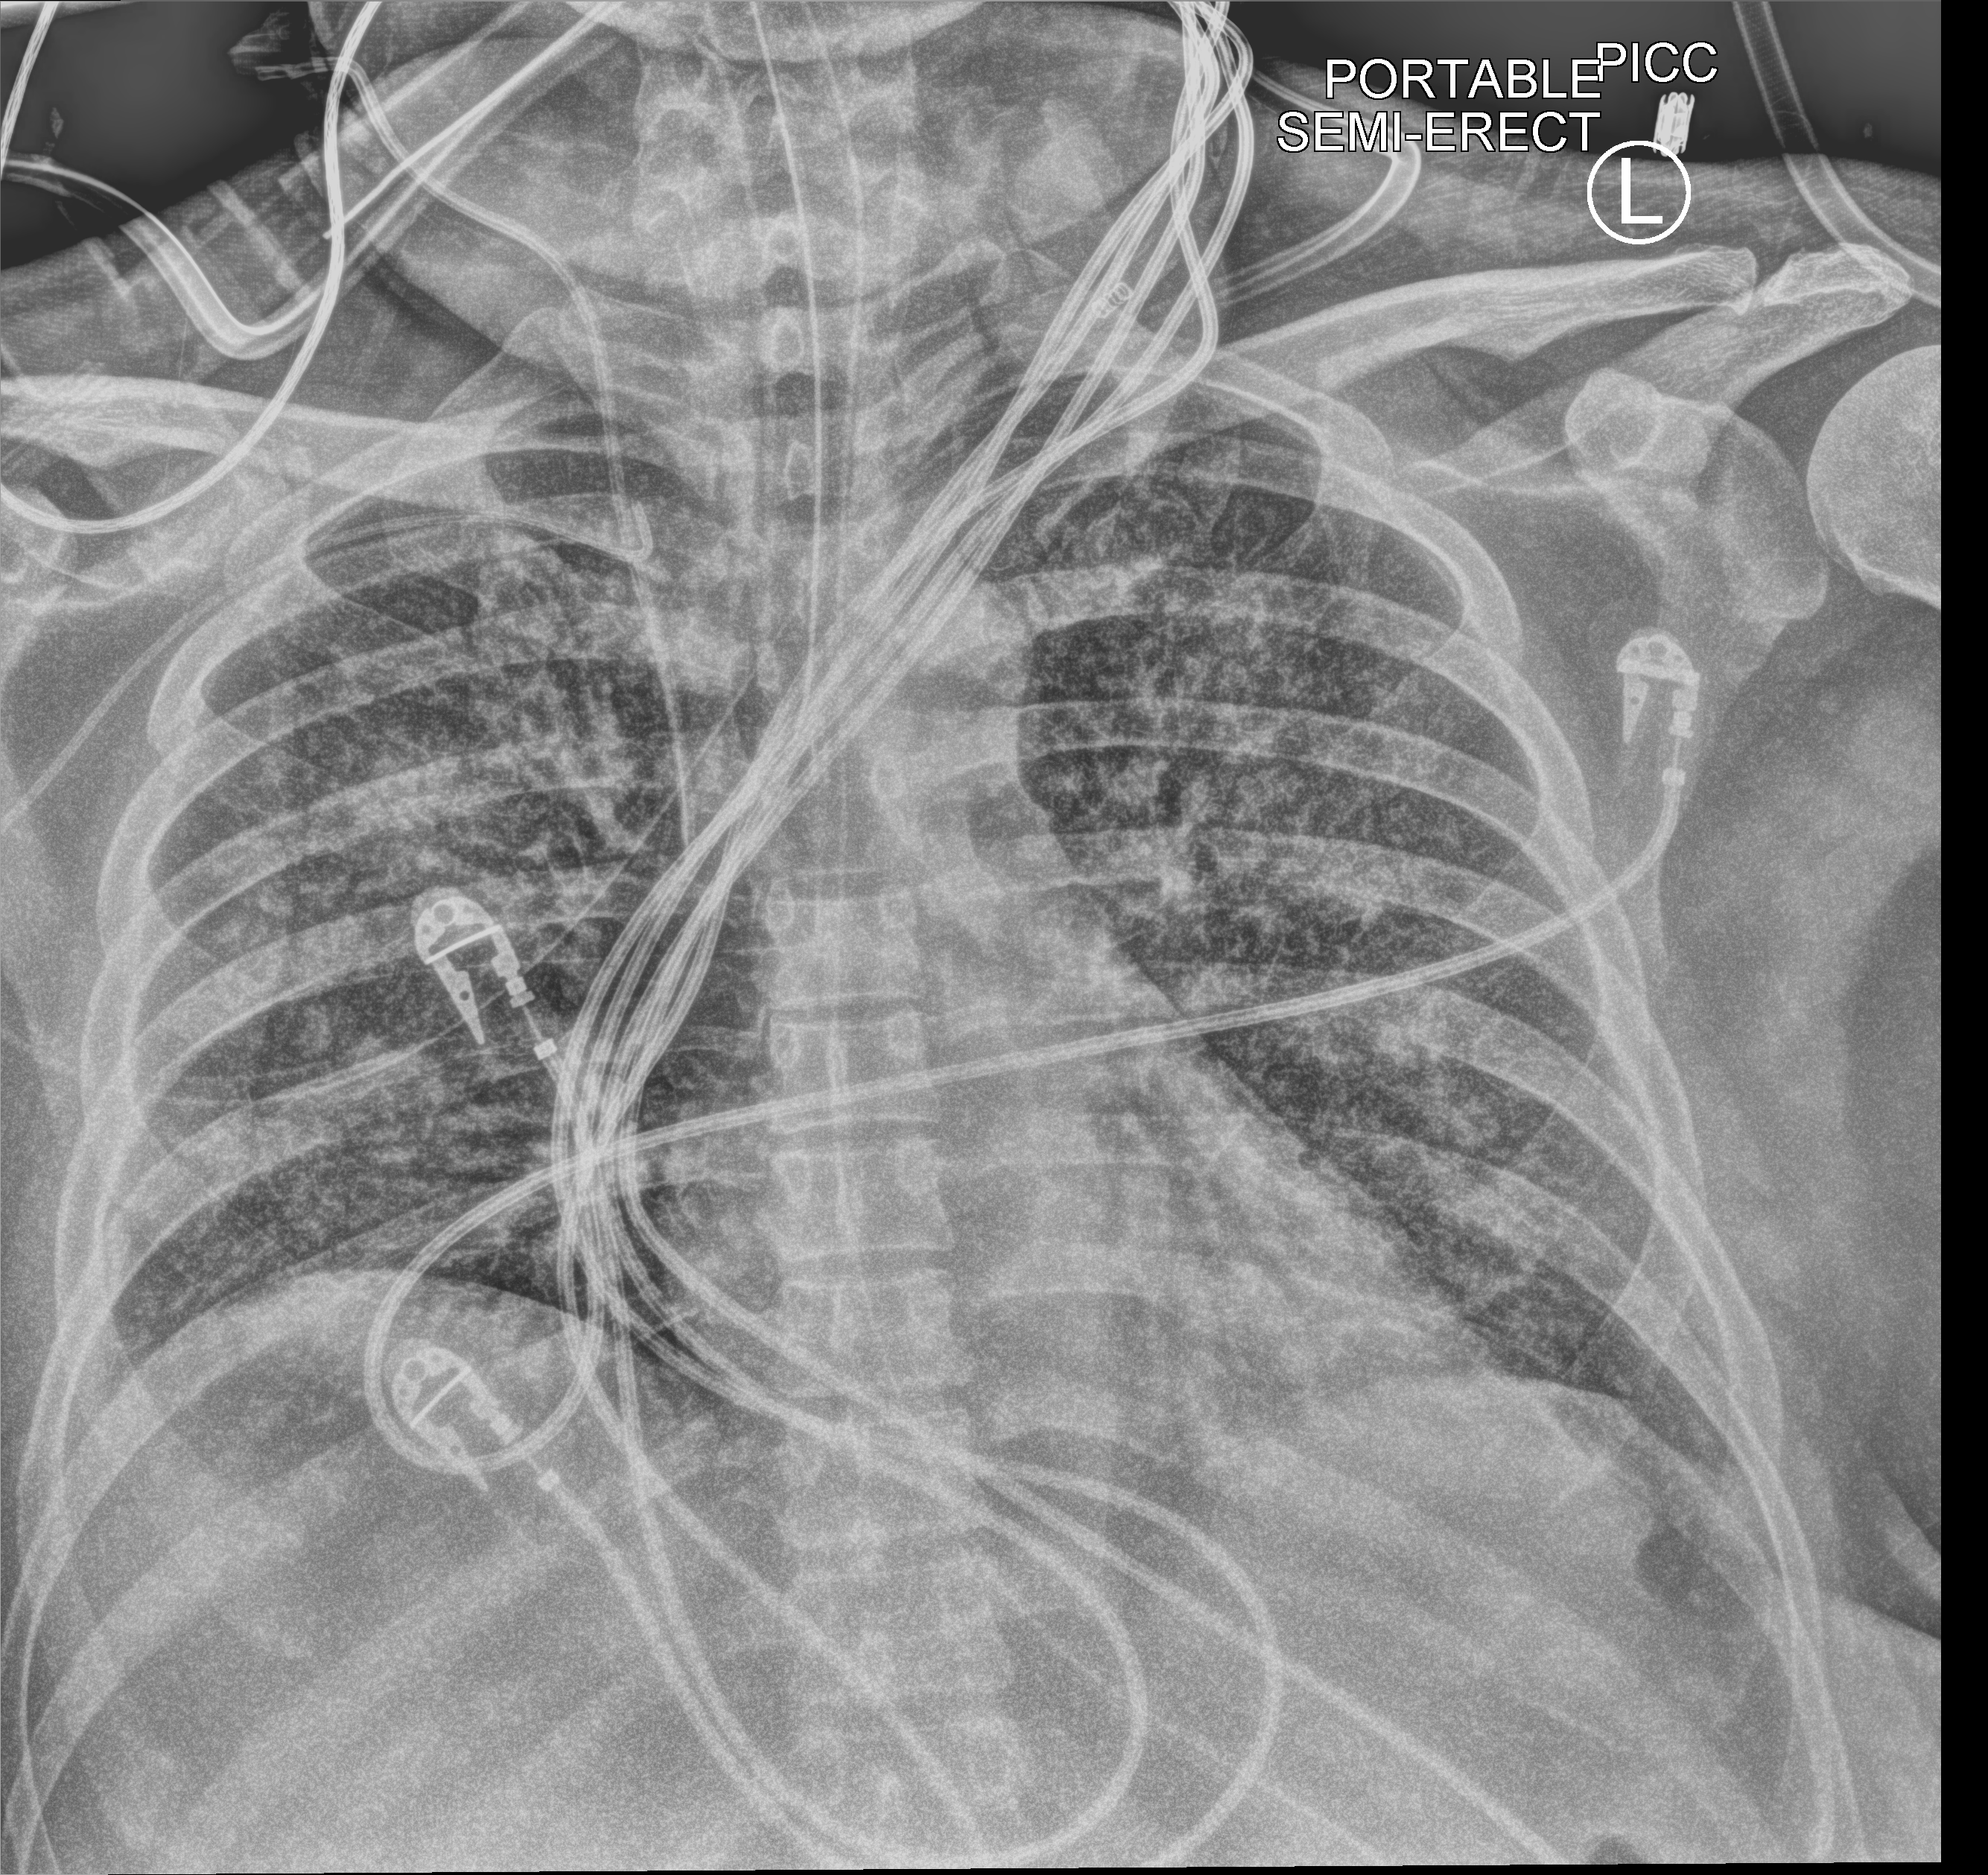
Chest X-ray (portable), anteroposterior (AP) projection. Patient hospitalised with COVID-19; male, aged 18–59 years.
Admission-level facts for this patient (not findings on this image; timing relative to this image not recorded): length of hospital stay: 96 days; smoking status (admission record): never.